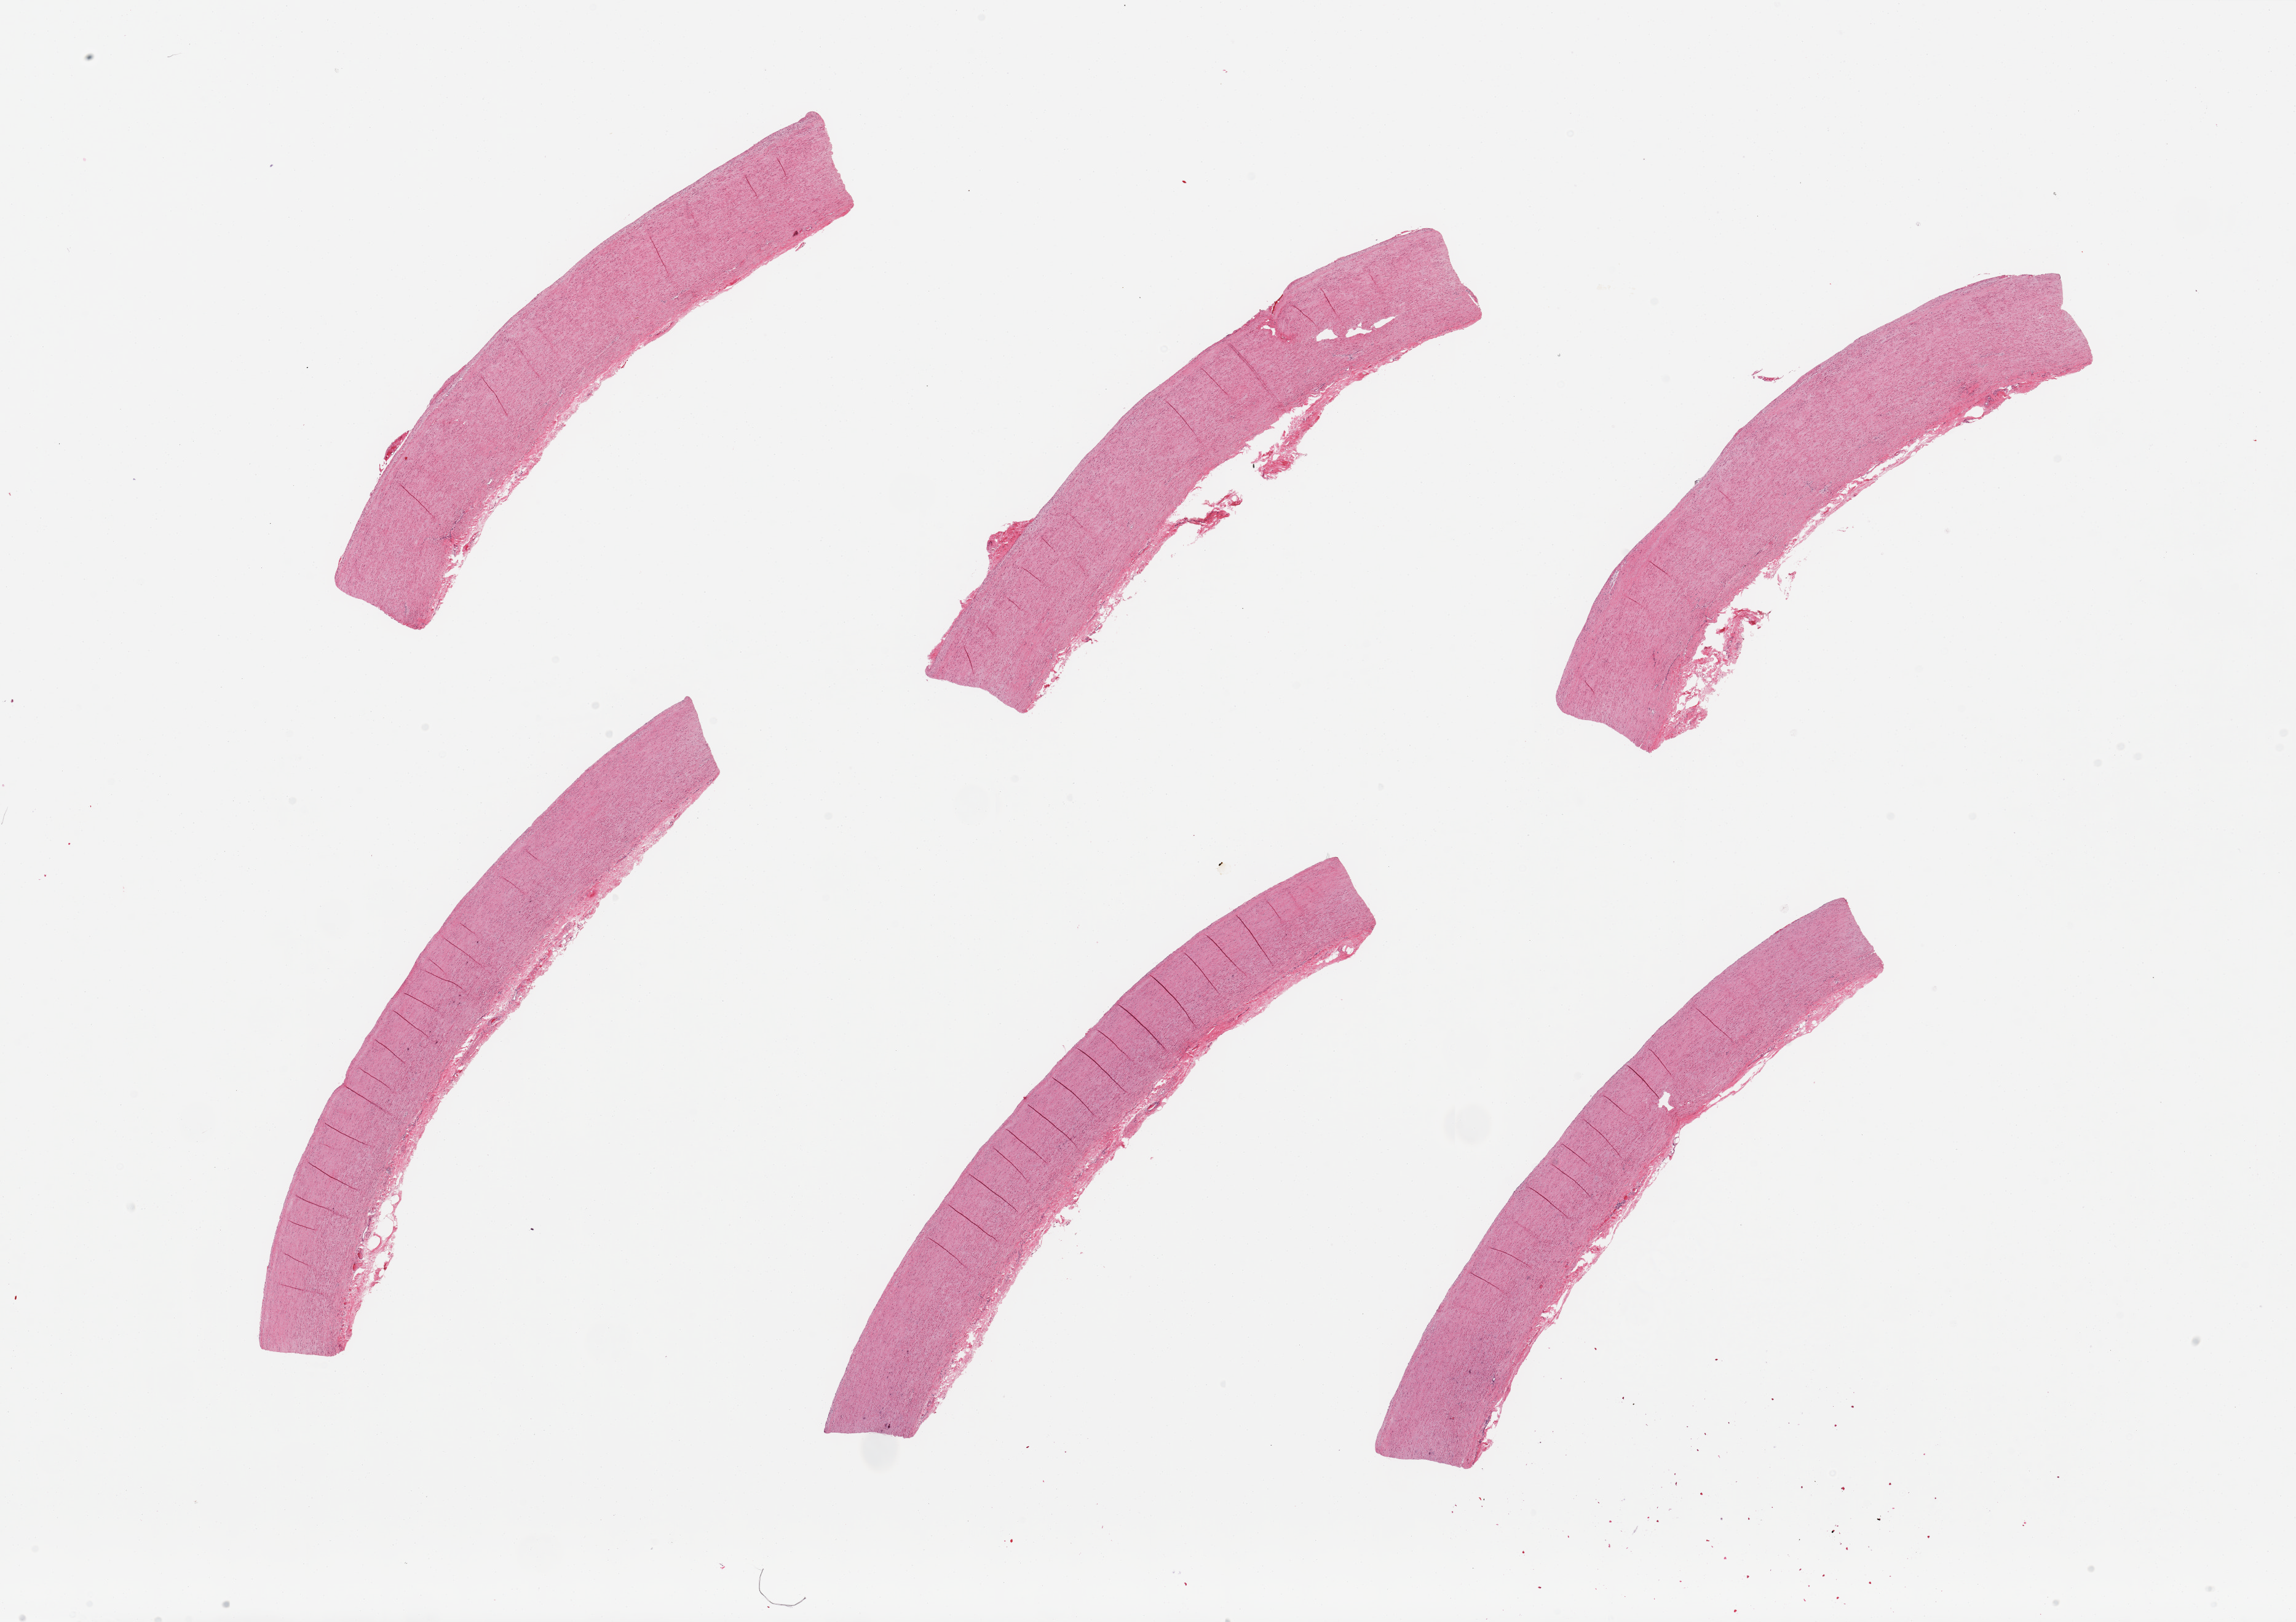
Digitized hematoxylin and eosin (H&E)-stained section — a low-resolution overview of the entire scanned area, about 29.5 x 20.9 mm (from a 20x scan), PAXgene-fixed paraffin-embedded (PFPE) section, sampled site (target tissue): aorta, tissue donor sample. Donor: male.
Reviewer comment on this tissue sample: 6 pieces; no plaques; well dissected.